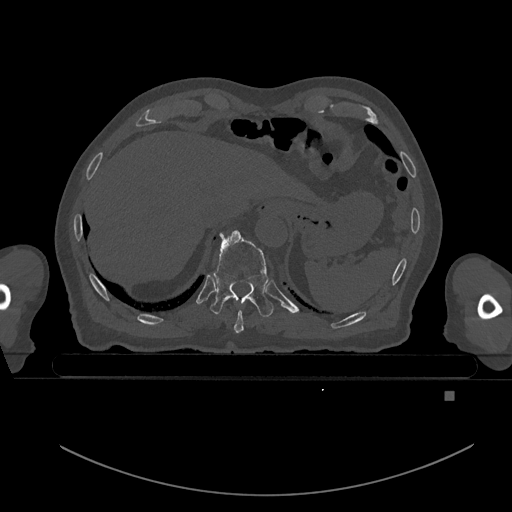
CT including the spine, one axial slice; position 103 of 969 along the scan axis; bone window (W 1800 / L 400 HU); 0.5 mm slice thickness; 512 × 512 image matrix, field of view 456 × 456 mm. Patient: male, 82 years. Case-level facts recorded for this patient, not image findings: primary cancer: prostate; vertebrae with lytic lesions (as recorded): T11, T9, T8, T2.
Structures marked on this image (semi-automatic segmentation, software-assisted and operator-edited):
- T10 vertebra: bounding box <211,230,273,317> (left, top, right, bottom; pixels)
- T9 vertebra: <234,310,244,333>